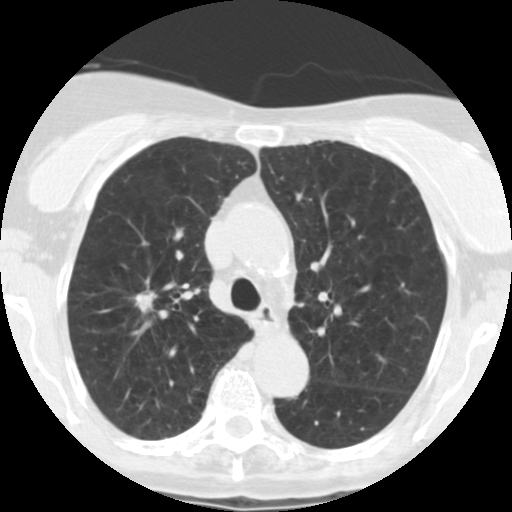
Low-dose screening chest CT, one axial slice. Position 173 of 246 along the scan axis. Reconstruction kernel STANDARD. 120 kVp. Lung window (W 1500 / L -600 HU). 512 × 512 image matrix, field of view 288 × 288 mm.
Structures marked on this image (manually delineated by an expert):
- lesion 1 (tumor, upper lobe of right lung): bounding box <134,290,157,314> (left, top, right, bottom; pixels)